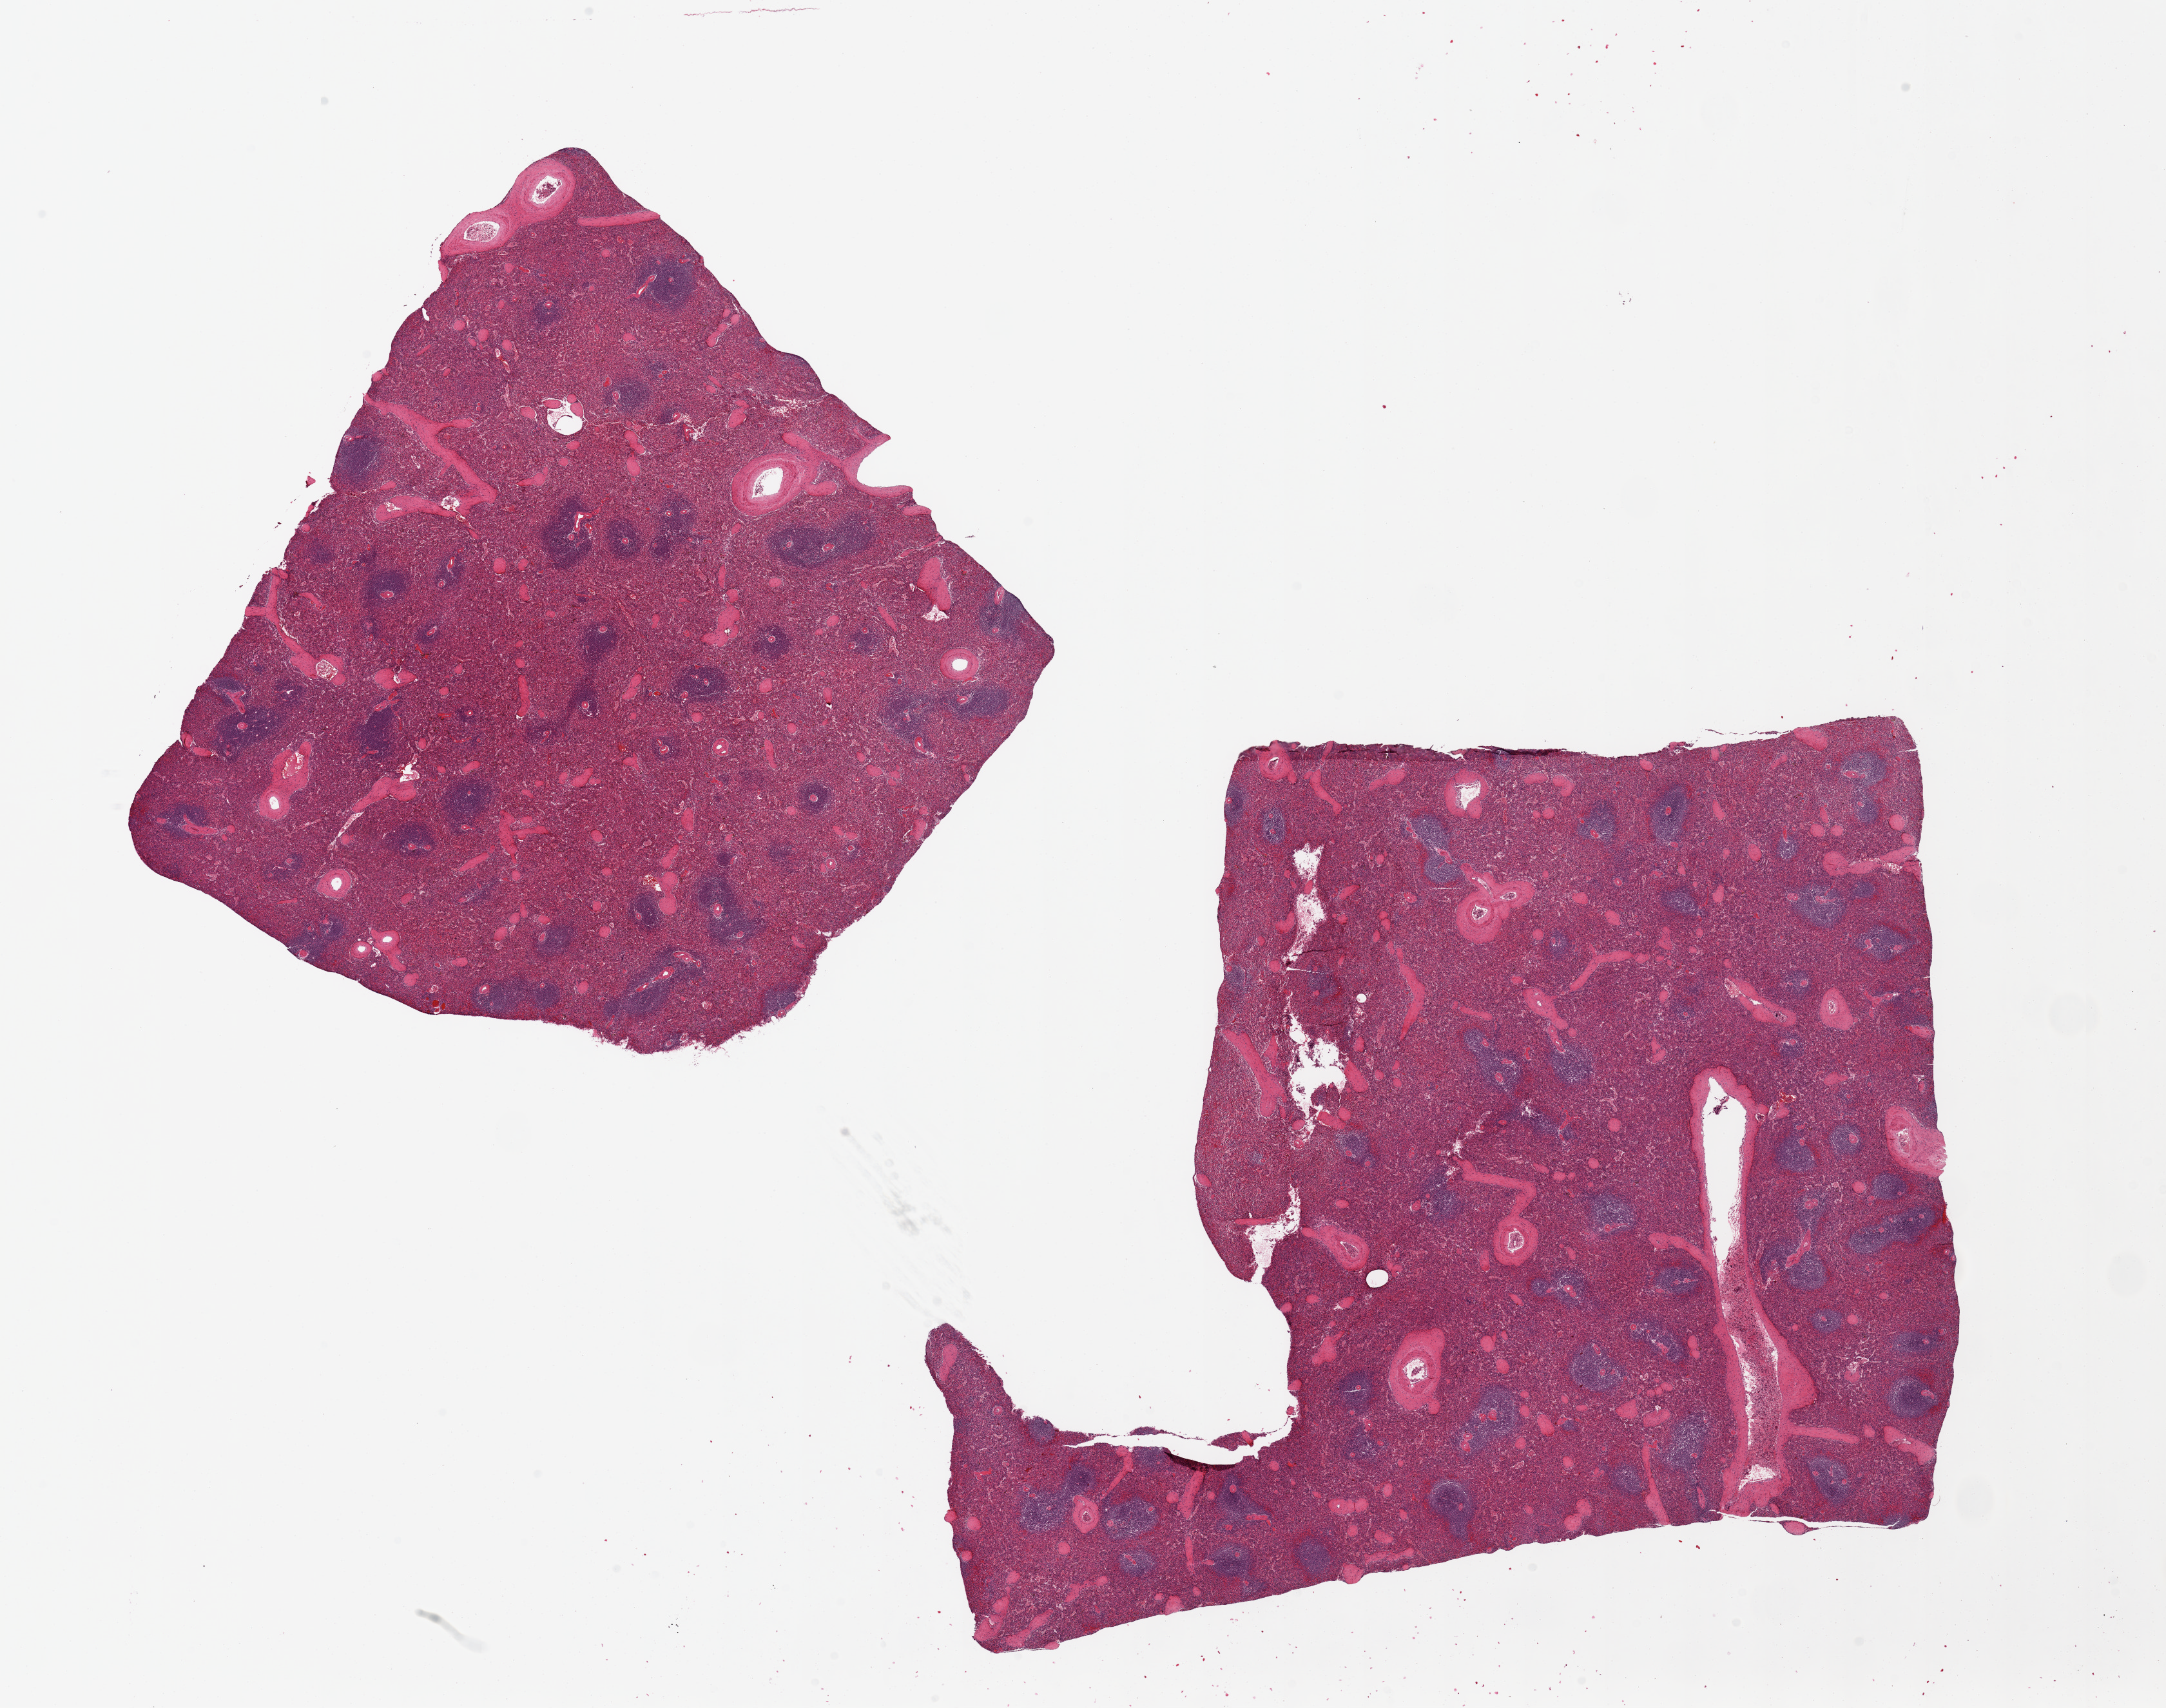
Whole-slide image, H&E stain — whole scanned area (about 26.6 x 21.0 mm) shown as a low-resolution overview, PAXgene-fixed, paraffin-embedded tissue, target tissue: spleen, tissue donor sample.
Review note (as recorded): 2 pieces.